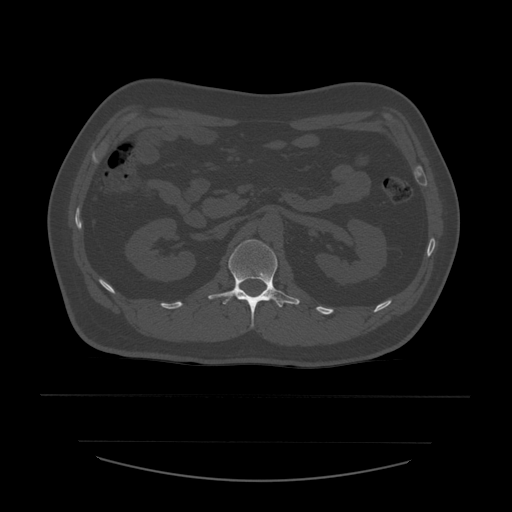
CT including the spine, one axial slice. Slice 225 of 532 in the series (ordered by position). Reconstruction kernel STANDARD. 120 kVp. Bone window (W 1800 / L 400 HU). 1.25 mm slice thickness. 512 × 512 image matrix, field of view 441 × 441 mm. Patient age 44 years. From the clinical record (not read from this slice): primary cancer: soft tissue sarcoma.
Structures marked on this image (semi-automatic segmentation, software-assisted and operator-edited):
- L1 vertebra: bounding box (x1, y1, x2, y2) in pixels: (208, 240, 300, 328)